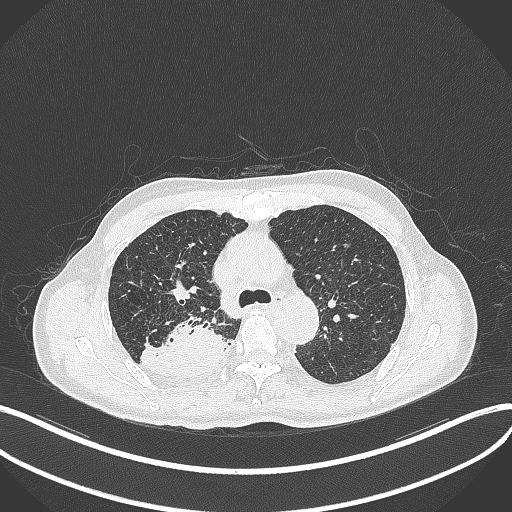
Chest CT, one axial slice; slice 314 of 428 in the series (ordered by position); reconstruction kernel B70f; lung window (W 1500 / L -600 HU); 1 mm slice thickness; 512 × 512 image matrix. Male patient, age 79 years. From the clinical record (not read from this slice): clinical TNM (as recorded): T3 N0 M0.
Outlined on this slice (rectangle marked by the reading radiologist):
- lung tumour (recorded histology: adenocarcinoma): bounding box [x1, y1, x2, y2] px = [139, 316, 226, 377]